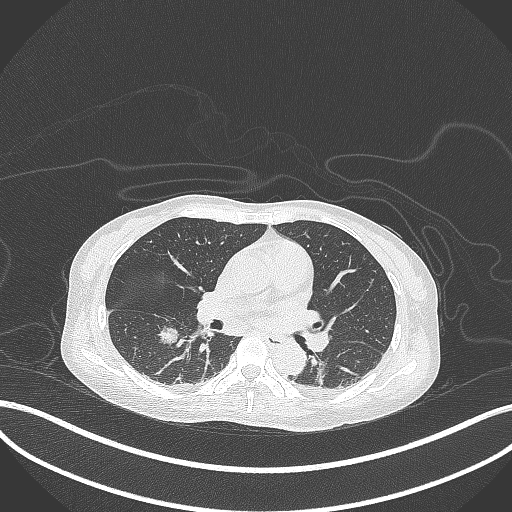
Chest CT, one axial slice. Slice 164 of 261 in the series (ordered by position). Reconstruction kernel B70f. 120 kVp. Lung window (W 1500 / L -600 HU). 1 mm slice thickness. 512 × 512 image matrix, field of view 400 × 400 mm. Female patient, age 44 years. Case-level facts recorded for this patient, not image findings: clinical TNM (as recorded): T1c N0 M0.
Outlined on this slice (bounding box drawn by a radiologist):
- lung tumour (recorded histology: adenocarcinoma): box from (x=156, y=325) to (x=180, y=348) px